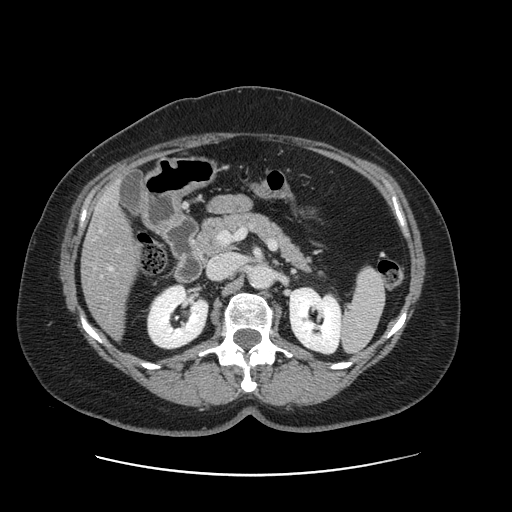
Contrast-enhanced abdominal CT, one axial slice. Slice 66 of 161 in the series (ordered by position). 120 kVp. Intravenous contrast given. Soft-tissue window (W 400 / L 40 HU). 512 × 512 image matrix, field of view 398 × 398 mm. Female patient, age 62 years. Case-level facts recorded for this patient, not image findings: diagnosis: colorectal cancer liver metastases, imaged before liver resection; multiple liver metastases: no; largest metastasis: 2.5 cm; disease in both lobes: no.
Annotated regions visible in this slice (expert manual segmentation):
- liver: box from (x=82, y=187) to (x=136, y=336) px